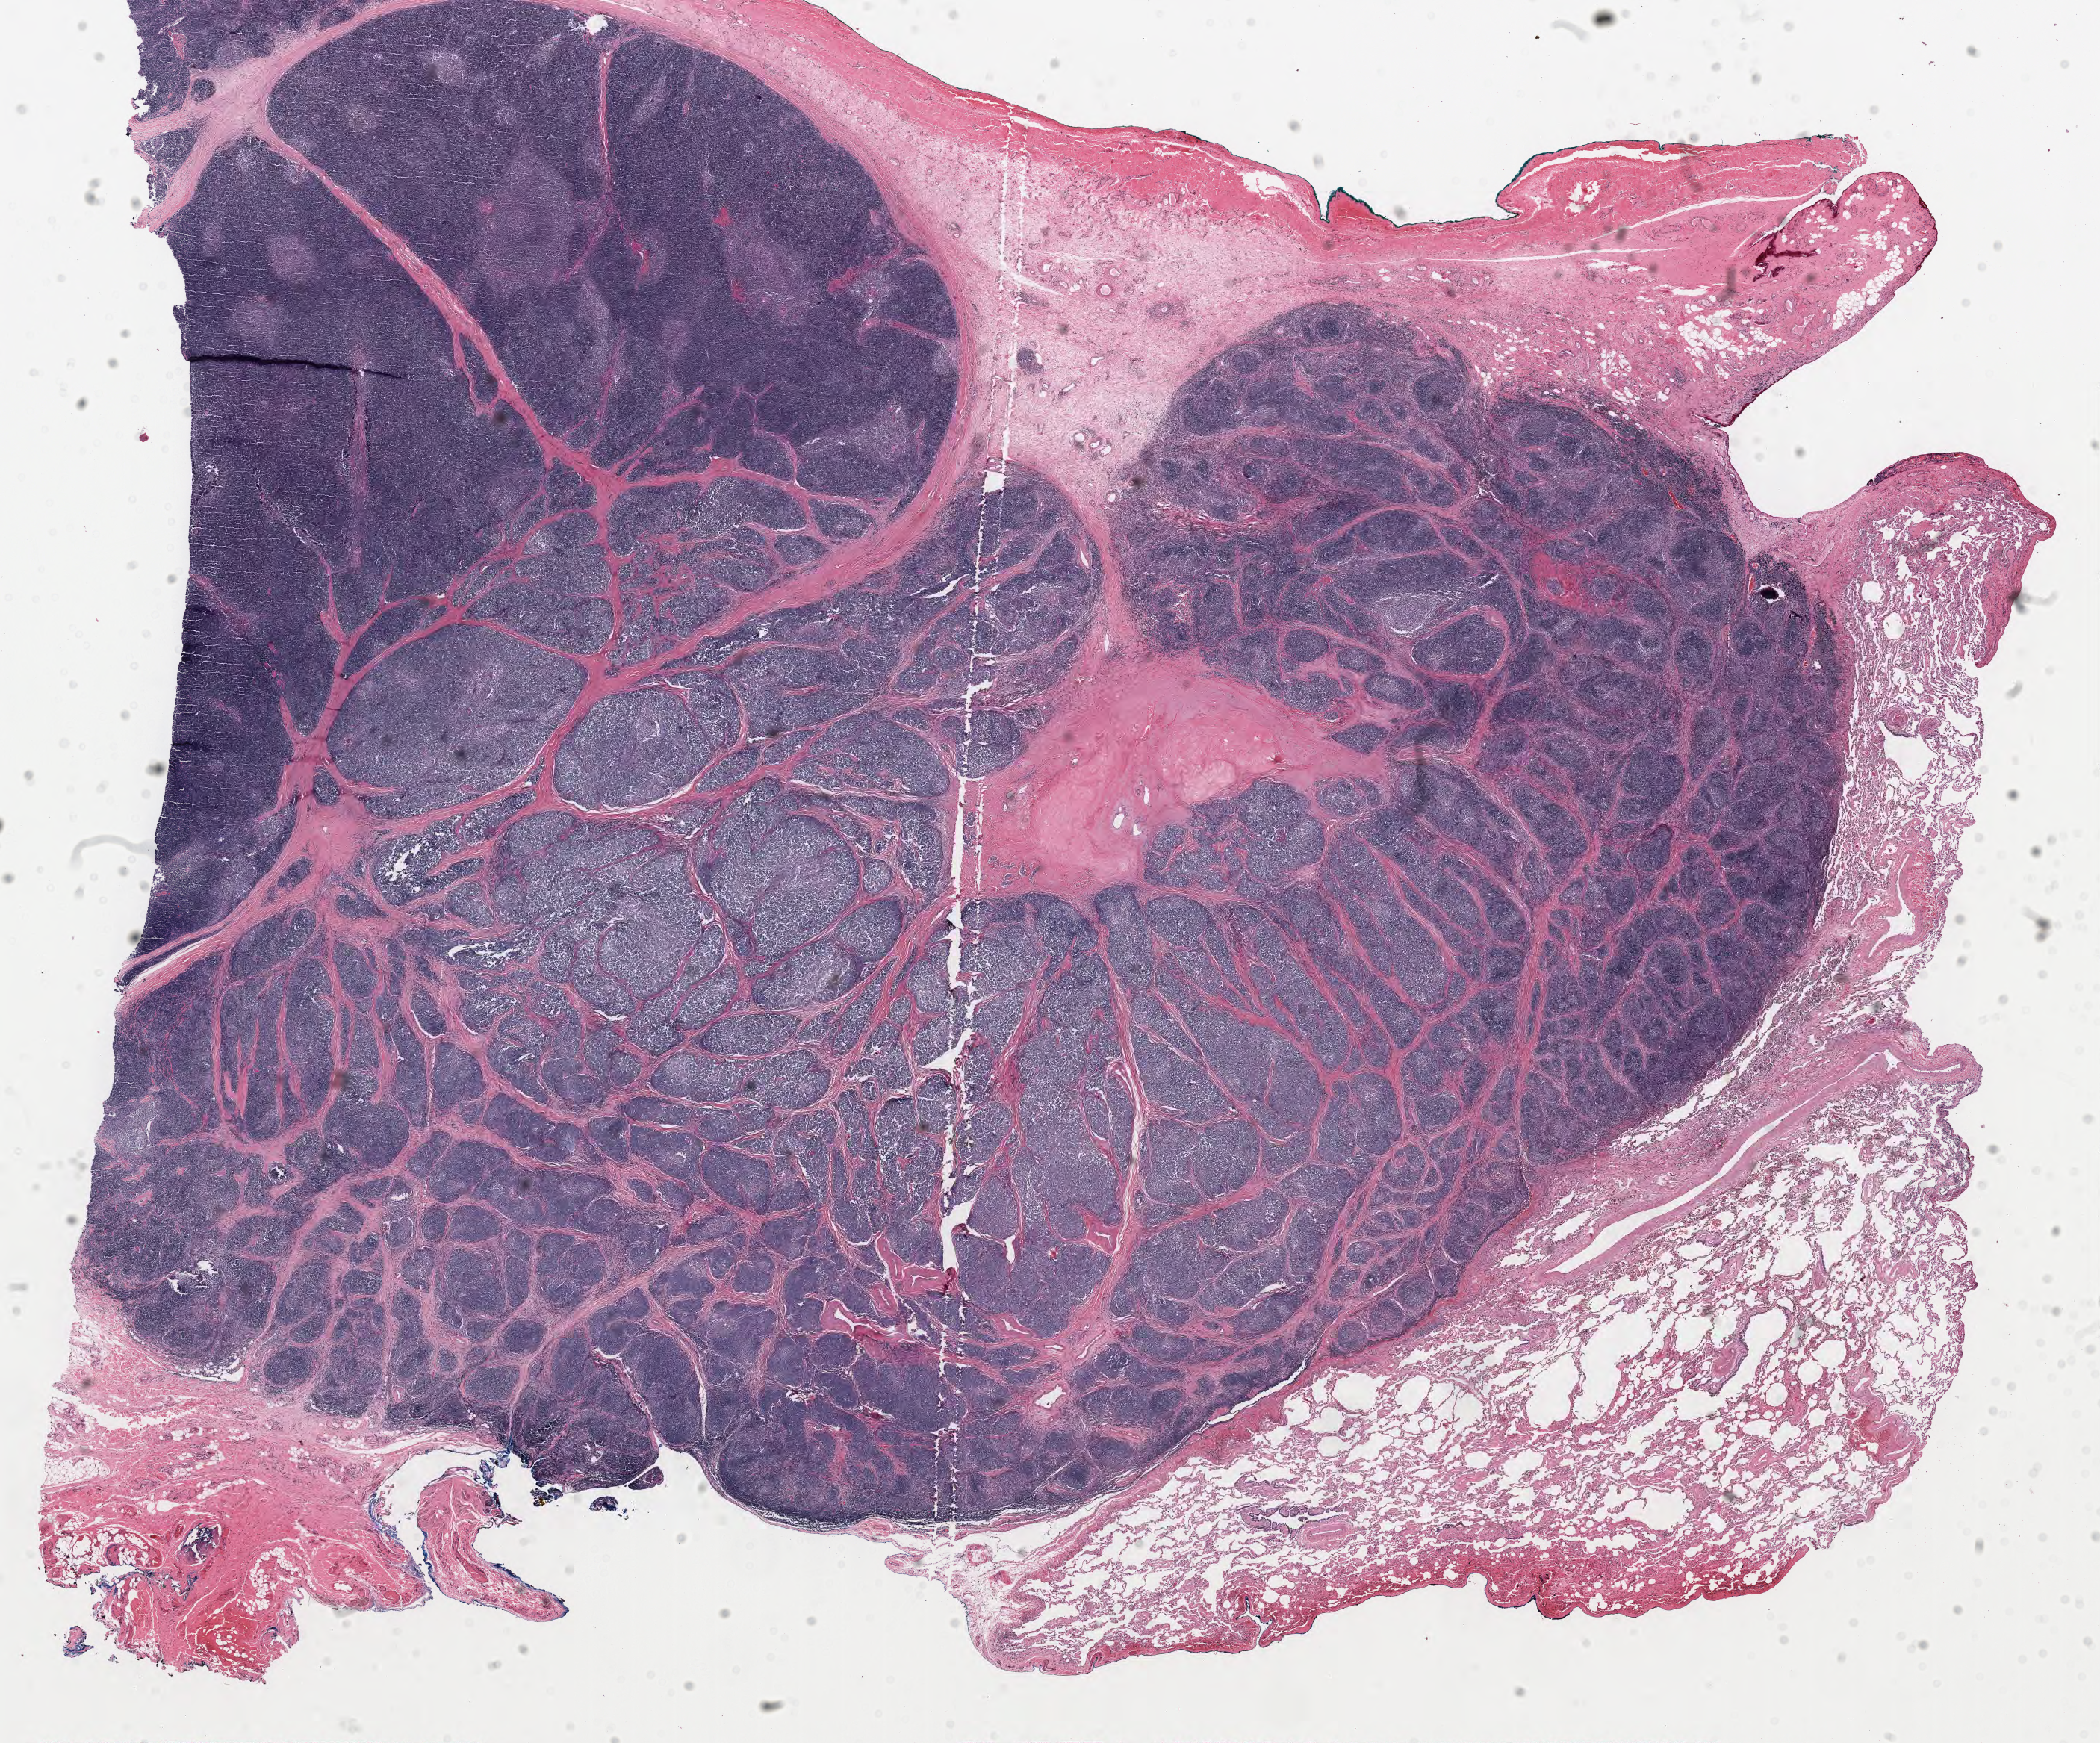
Digitized H&E-stained tissue section (whole slide), shown as a low-resolution overview of the whole scanned area (about 22.3 x 18.5 mm, acquisition: 40x scan); FFPE section; thymus, primary tumour sample. Female, age 57 years at initial diagnosis.
Diagnosis: Thymoma, type B1, NOS.